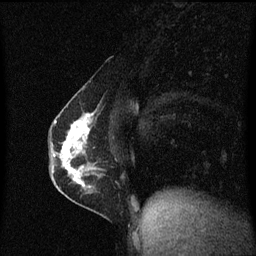
Breast MRI (dynamic contrast-enhanced), one sagittal slice. Position 27 of 60 along the scan axis. Dynamic contrast-enhanced series, image 2 of 3 at this slice position (ordered by acquisition). 1.5 T. TE 4.2 ms, TR 8.4 ms. 2 mm slice thickness. 256 × 256 image matrix, field of view 200 × 200 mm. Patient: female, 40 years.
Structures marked on this image (semi-automatically segmented with operator editing):
- analysis volume of interest (the breast-tissue region the enhancement analysis was run in; not a lesion): box from (x=57, y=110) to (x=104, y=191) px
- tumour enhancement mask (voxels above the 70 % enhancement threshold inside the analysis volume of interest): (x=60, y=114)–(x=95, y=189)